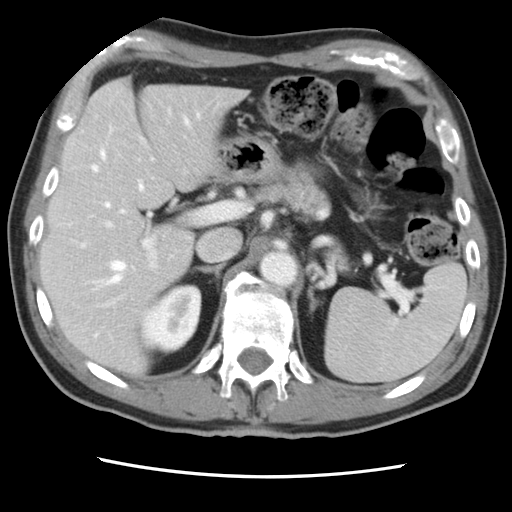
Contrast-enhanced abdominal CT, one axial slice. Slice 53 of 83 in the series (ordered by position). 120 kVp. Intravenous contrast given. Soft-tissue window (W 400 / L 40 HU). 5 mm slice thickness. 512 × 512 image matrix. Male patient, age 69 years. Case-level facts recorded for this patient, not image findings: diagnosis: colorectal cancer liver metastases, imaged before liver resection; multiple liver metastases: yes; largest metastasis: 3.5 cm; disease in both lobes: no.
Annotated regions visible in this slice (expert manual segmentation):
- hepatic veins: bounding box (x1, y1, x2, y2) in pixels: (93, 118, 189, 337)
- liver: (43, 80, 242, 373)
- planned liver remnant (the part of the liver to remain after resection): (43, 137, 194, 373)
- portal vein (with intrahepatic branches): (80, 135, 231, 307)